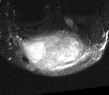
MRI of an extremity soft-tissue mass, one axial slice. Position 17 of 52 along the scan axis. T2-weighted fat-saturated. MR volume resampled by the dataset authors to the PET/CT grid (not the native acquisition matrix). 3.27 mm slice thickness. 109 × 95 image matrix, field of view 106 × 93 mm. Male patient. Case-level facts recorded for this patient, not image findings: histological type: synovial sarcoma; site of the primary tumour: left poplietal fossa.
Structures marked on this image (expert contour drawn on MRI and transferred to this co-registered scan by the dataset authors):
- gross tumour volume (mass): bounding box (x1, y1, x2, y2) in pixels: (19, 29, 86, 71)